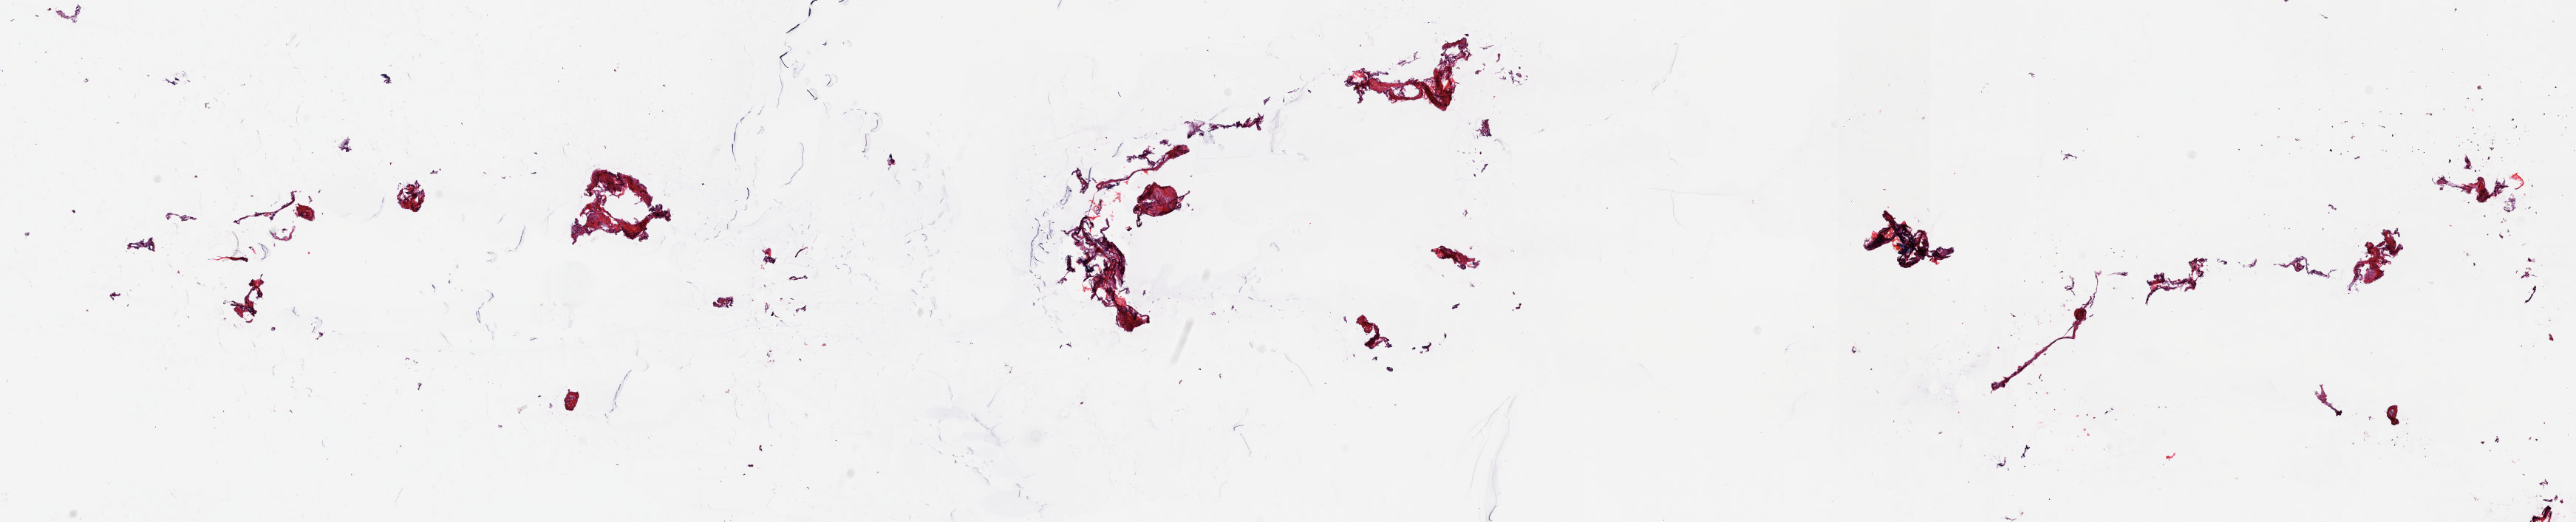
Digitized H&E tissue section (whole slide) — shown as a low-resolution overview of the whole scanned area (about 27.7 x 5.6 mm, acquisition: 20x scan); frozen section from the top of the tissue portion; solid tissue normal (non-tumour tissue) sample from the uterus. Female, age 63 years at initial diagnosis. Pathologist review of this section (percent, as recorded): tumour cells 0%, tumour nuclei 0%, normal cells 100%, stromal cells 0%, necrosis 0%. Inflammatory infiltration, as recorded: lymphocyte infiltration 40%, monocyte infiltration 20%, neutrophil infiltration 20%.
This section: solid tissue normal sample (biorepository sample class). Patient diagnosis: Serous cystadenocarcinoma, NOS (endometrium).